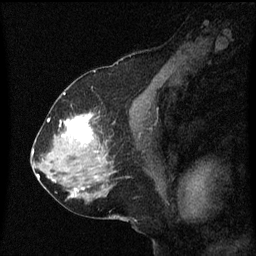
Breast MRI (dynamic contrast-enhanced), one sagittal slice. Slice 33 of 60 in the series (ordered by position). Dynamic contrast-enhanced series, image 2 of 3 at this slice position (ordered by acquisition). 1.5 T. TE 4.2 ms, TR 8.4 ms. 256 × 256 image matrix, field of view 200 × 200 mm. Patient: female, 58 years.
Outlined on this slice (semi-automatic segmentation, software-assisted and operator-edited):
- analysis volume of interest (the breast-tissue region the enhancement analysis was run in; not a lesion): bounding box <58,114,99,151> (left, top, right, bottom; pixels)
- tumour enhancement mask (voxels above the 70 % enhancement threshold inside the analysis volume of interest): <62,114,95,143>